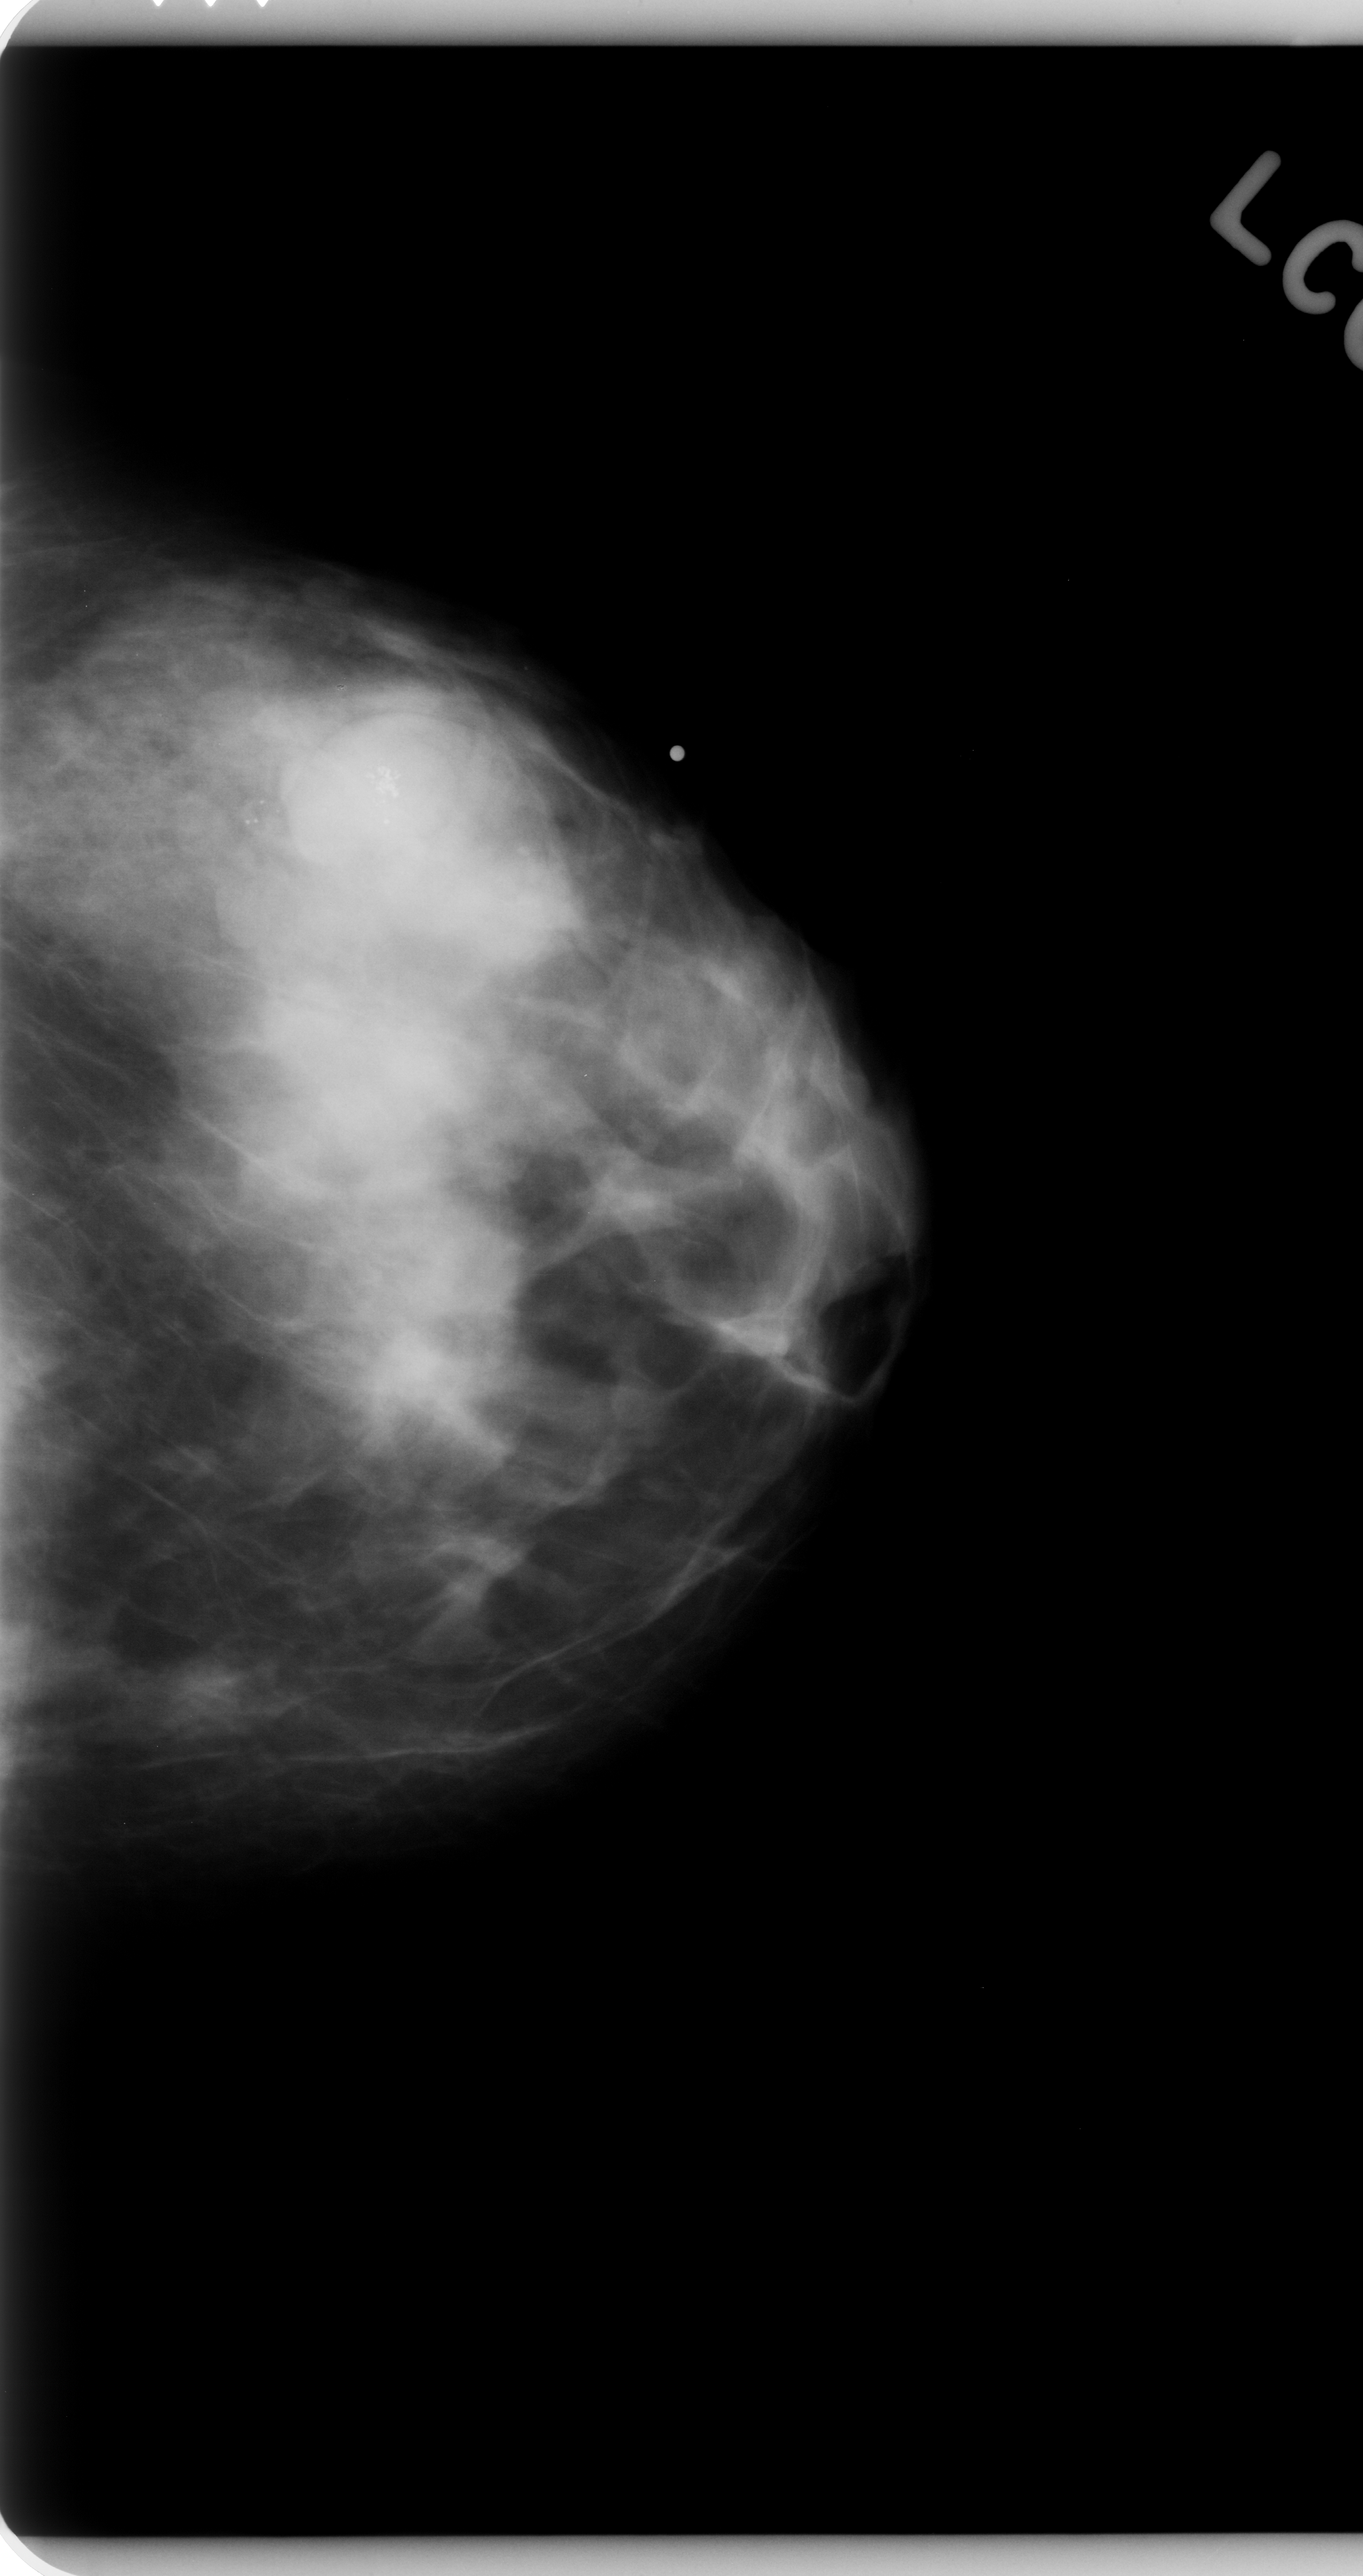
Scanned film-screen mammogram; left breast; craniocaudal (CC) view; BI-RADS breast density category 3 (scale 1–4).
Finding: mass, shape lobulated, margins obscured; BI-RADS assessment category 3; subtlety rating 3 on a 1 (subtle) to 5 (obvious) scale; pathology result (as recorded, not read from the image): benign.